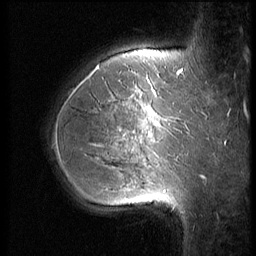
Breast MRI (dynamic contrast-enhanced), one sagittal slice. Slice 46 of 56 in the series (ordered by position). 3 images stored at this slice position (order not interpretable as contrast timing). 1.5 T. TE 4.2 ms, TR 9 ms. 2.5 mm slice thickness. 256 × 256 image matrix, field of view 180 × 180 mm. Patient: female, 35 years. Case-level facts recorded for this patient, not image findings: setting: breast cancer imaged before/during neoadjuvant chemotherapy; receptor status: HR-positive, HER2-negative.
Structures marked on this image (semi-automatic segmentation, software-assisted and operator-edited):
- analysis volume of interest (the breast-tissue region the enhancement analysis was run in; not a lesion): bounding box <63,60,190,218> (left, top, right, bottom; pixels)
- tumour enhancement mask (voxels above the 140 % enhancement threshold inside the analysis volume of interest): <98,66,158,125>